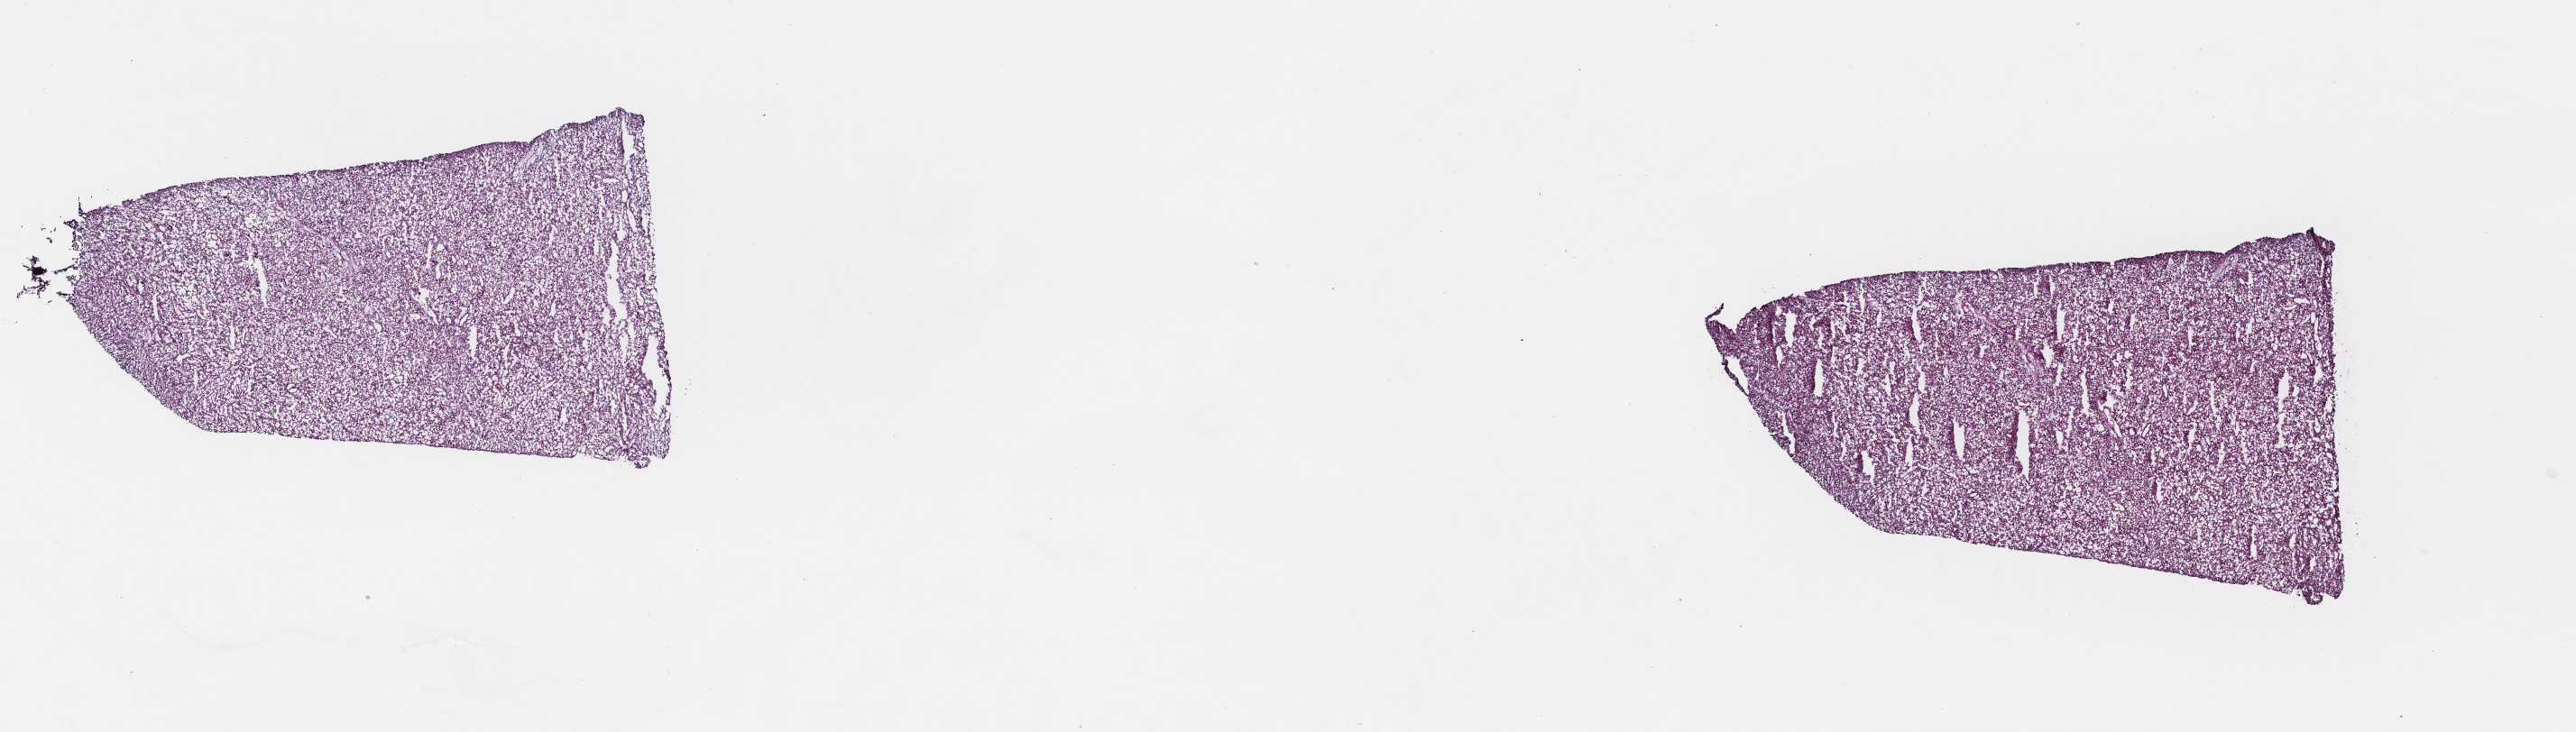
Whole-slide histology image, H&E — shown as a low-resolution overview of the whole scanned area (about 22.4 x 6.4 mm, from a 40x scan); frozen section from the top of the tissue portion; sample: primary tumour, adrenal cortex. Male patient; age at initial diagnosis 48 years. Pathologist review of this section (percent, as recorded): tumour cells 95%, tumour nuclei 100%, normal cells 0%, stromal cells 5%, necrosis 0%. Inflammatory infiltration, as recorded: lymphocyte infiltration 0%, monocyte infiltration 0%, neutrophil infiltration 0%.
Pathologic diagnosis: Adrenal cortical carcinoma (cortex of adrenal gland).